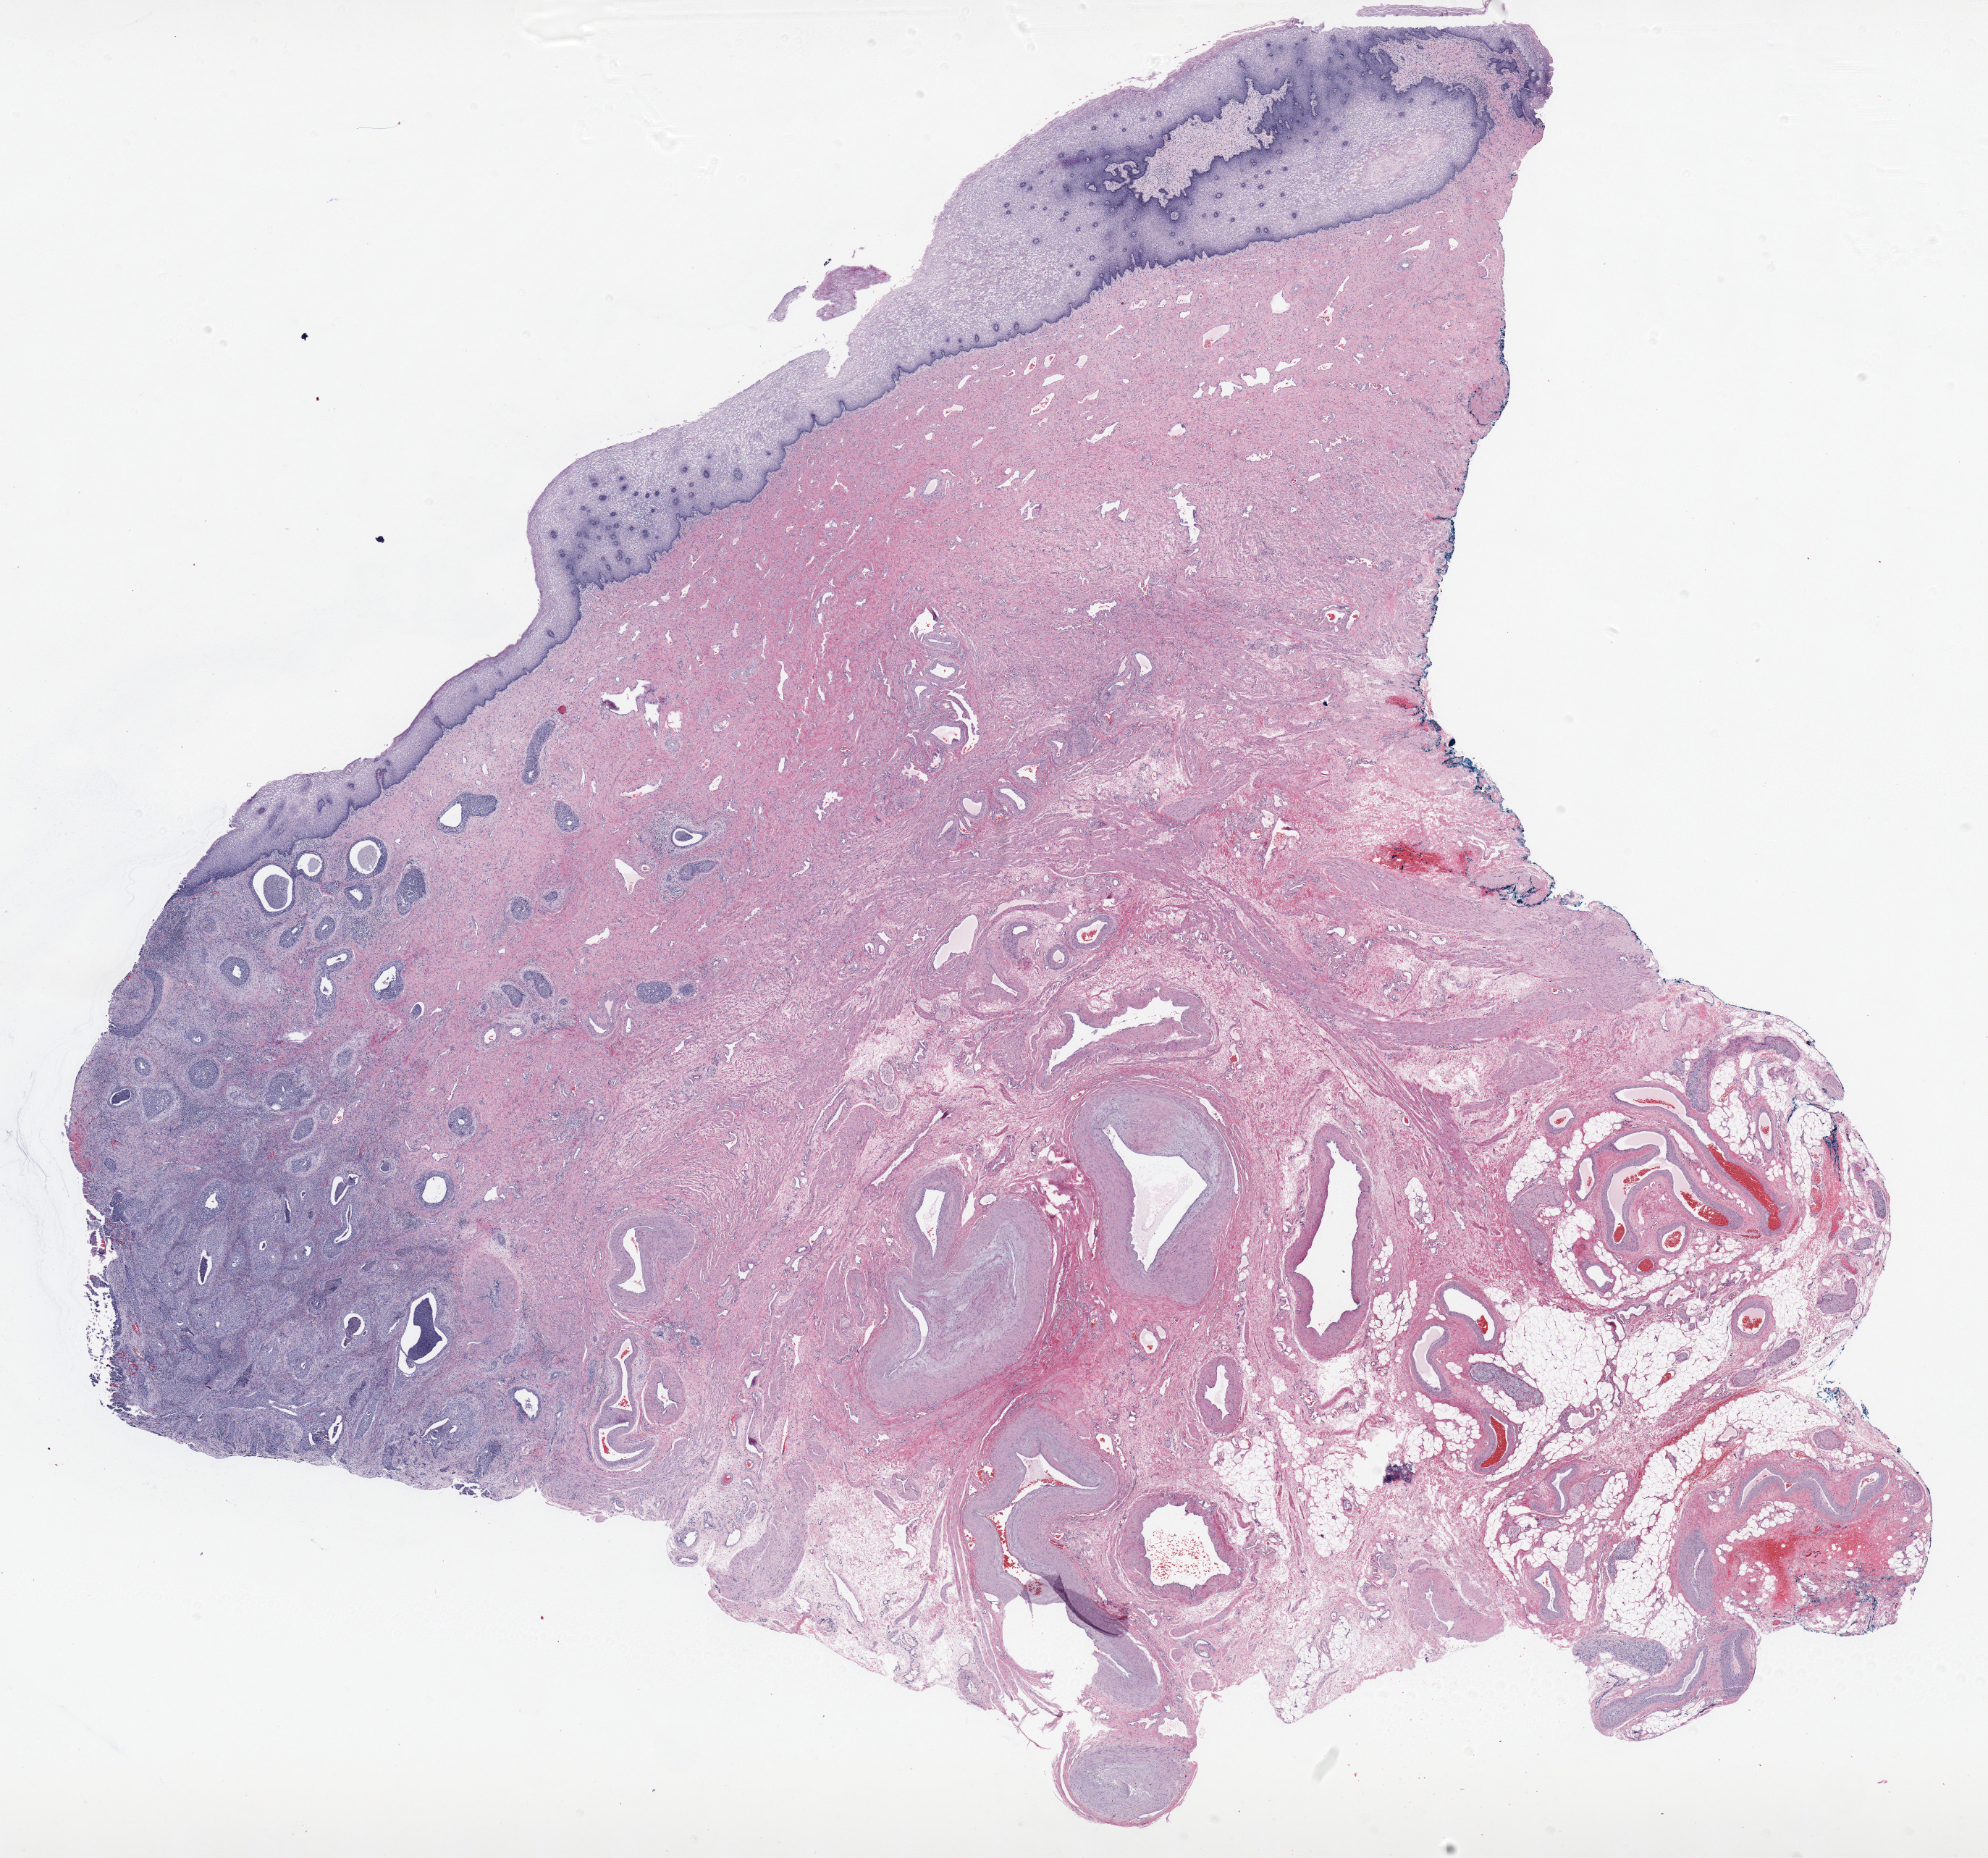
Whole-slide histology image, H&E — low-resolution overview of the scanned area, about 21.9 x 20.4 mm (from a 20x scan), FFPE section, cervix, primary tumour sample. Female patient; age at initial diagnosis 37 years. Histologic grade: G3 (poorly differentiated).
FIGO stage: IB1. Lymph nodes positive (case pathology): 0 of 20 examined. Pathologic diagnosis: Squamous cell carcinoma, NOS (cervix uteri).